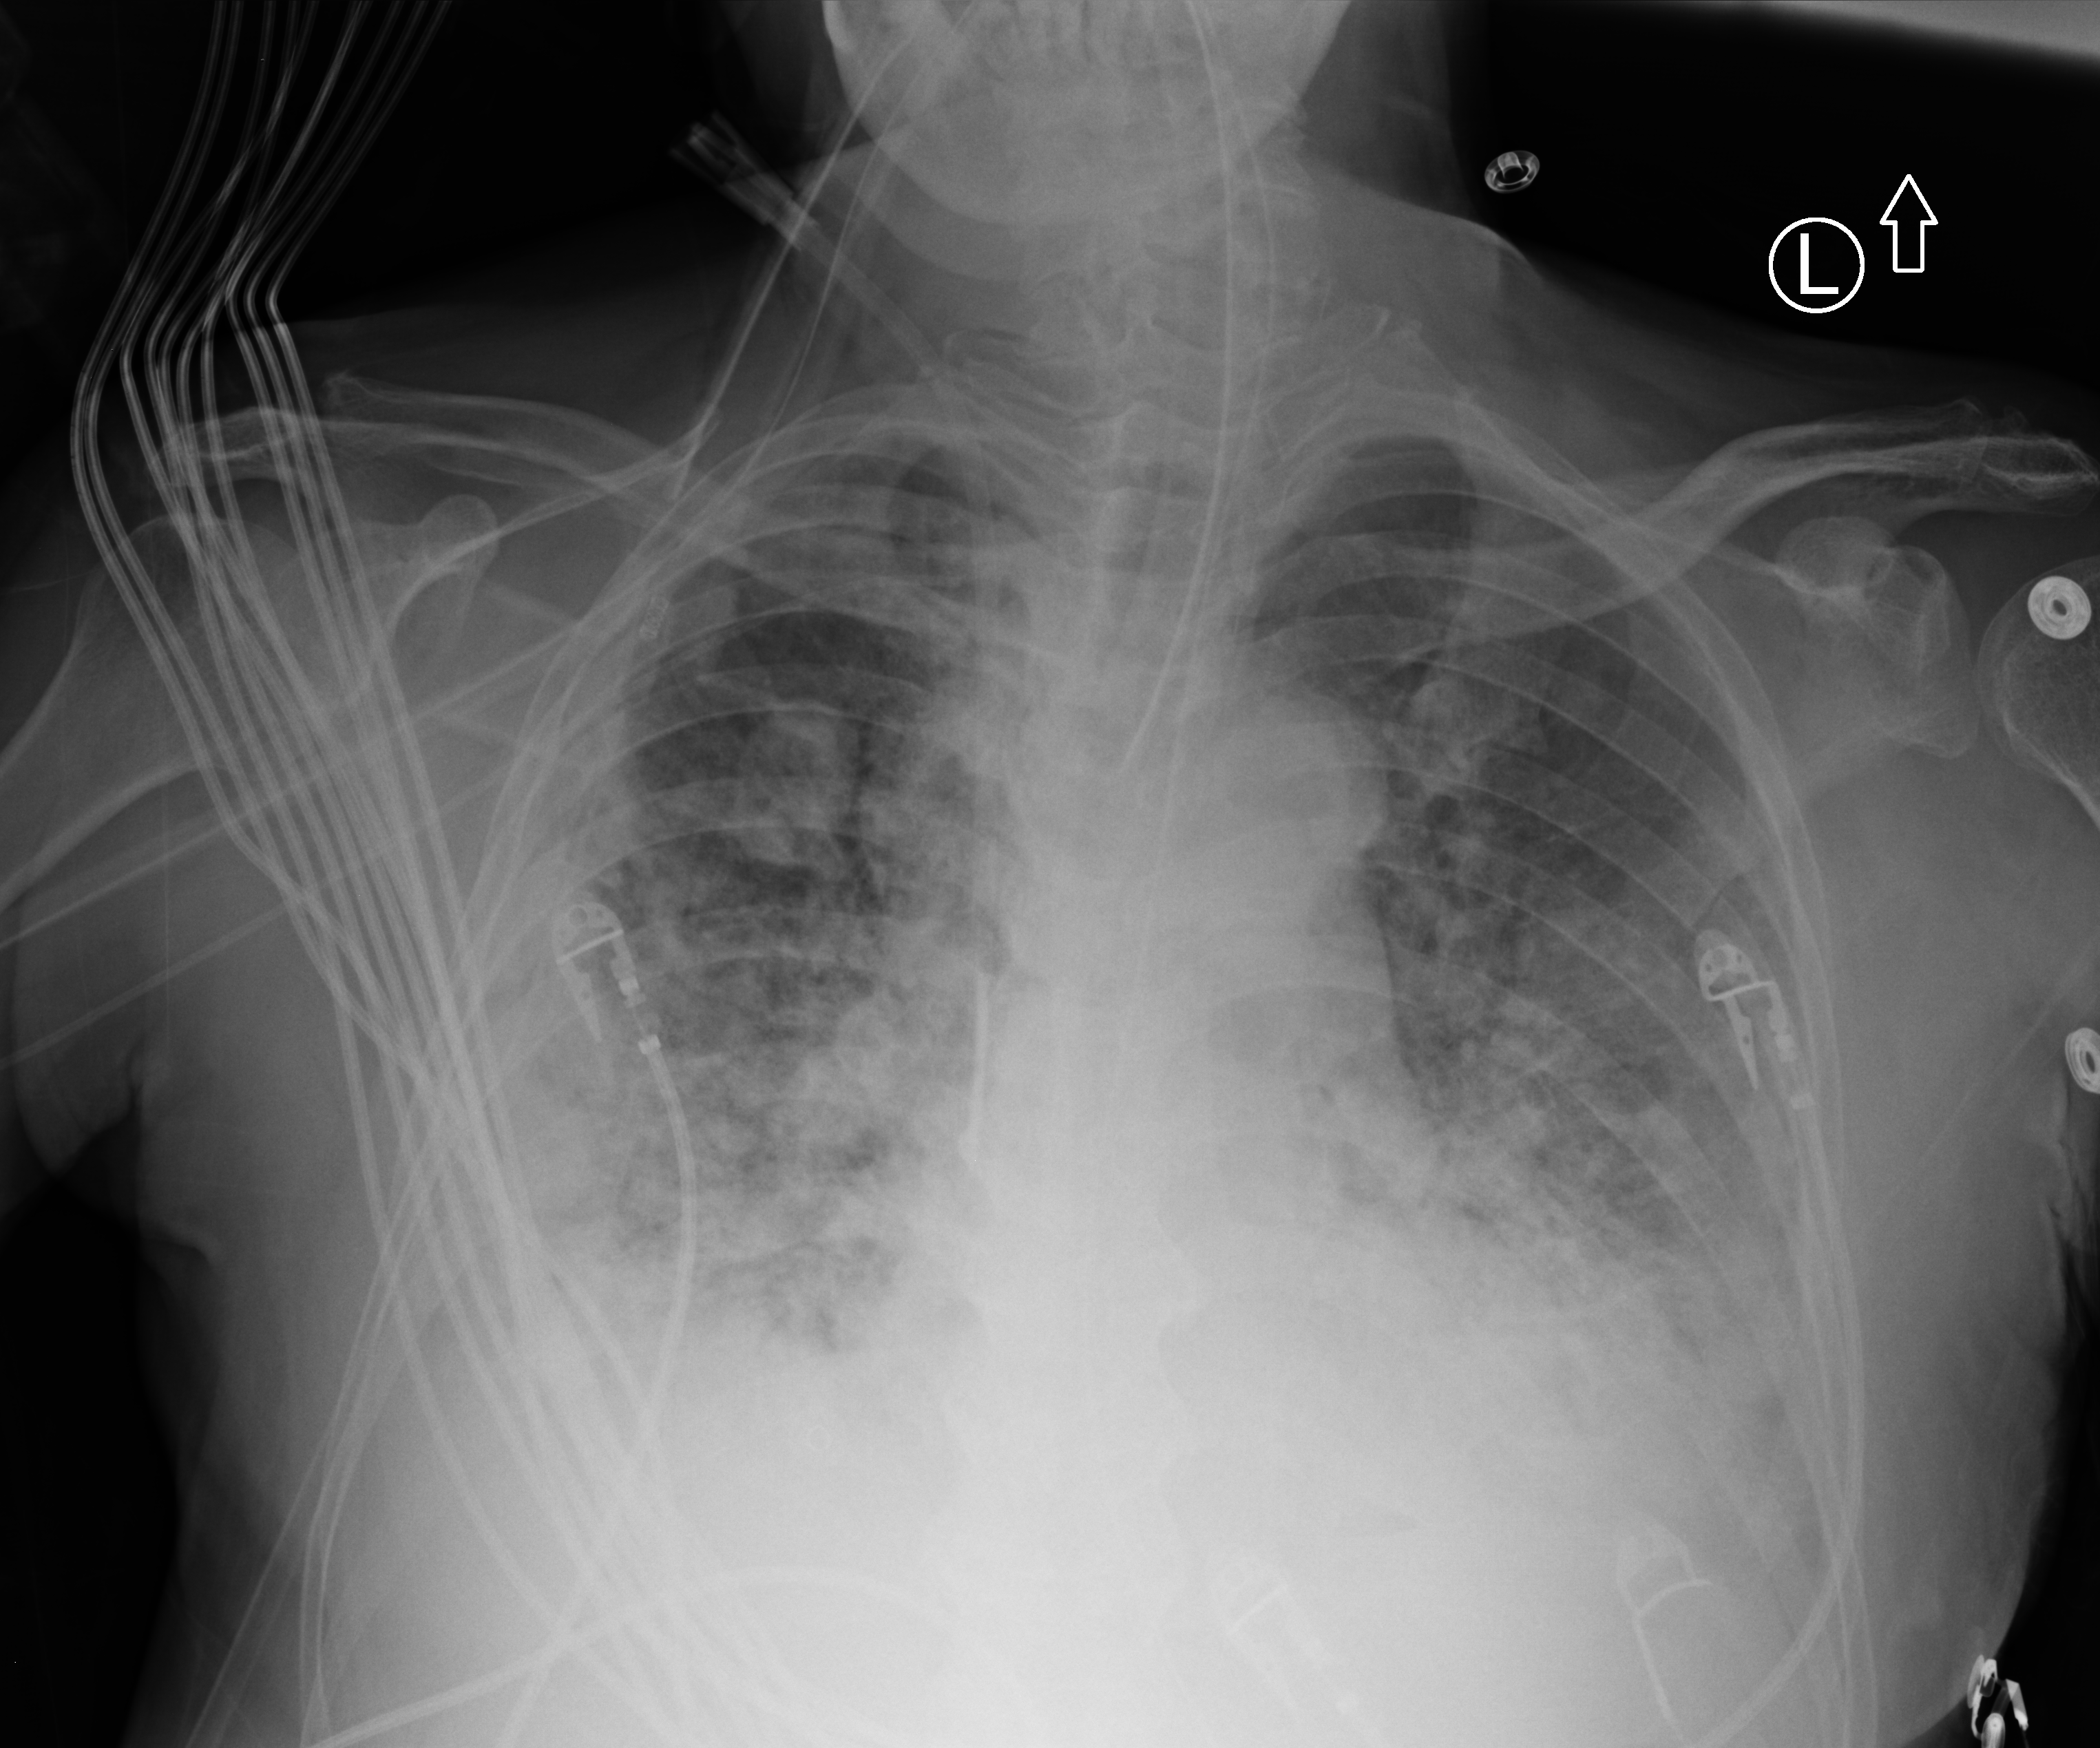
Chest X-ray (portable); anteroposterior (AP) projection. Patient hospitalised with COVID-19; male, aged 60–74 years.
Admission-level facts for this patient (not findings on this image; timing relative to this image not recorded): smoking status (admission record): never.